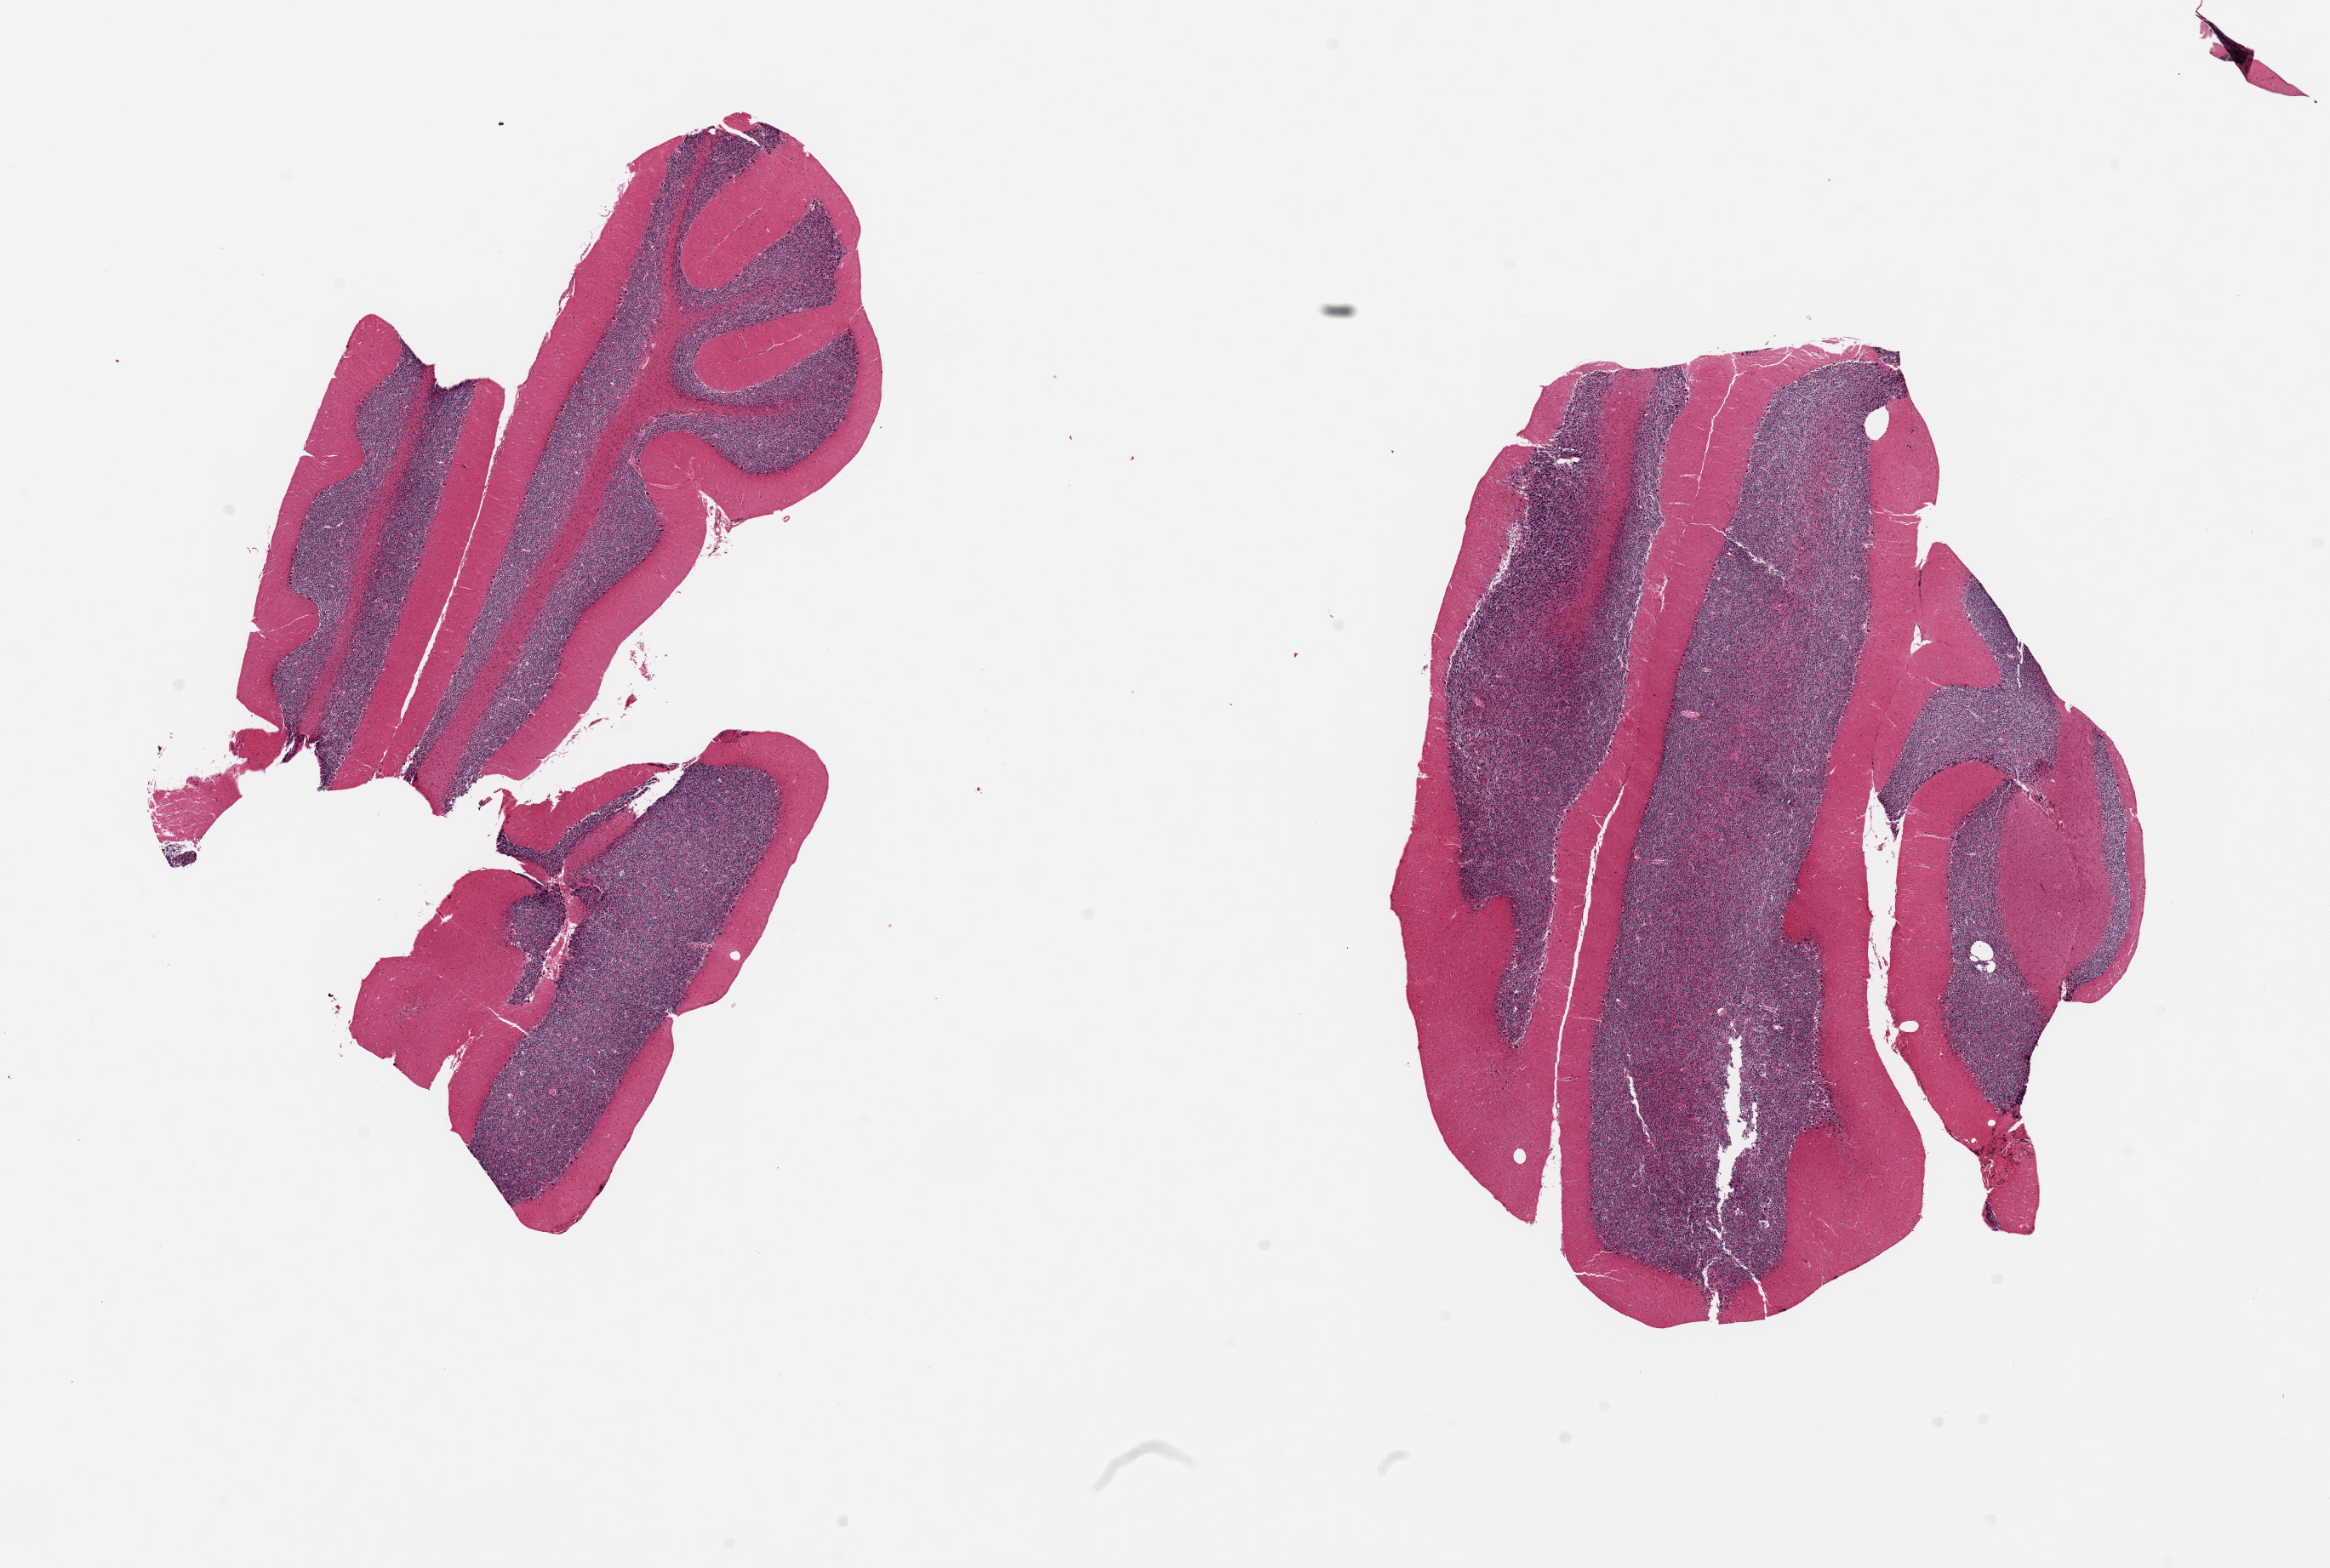
Whole-slide image, haematoxylin and eosin stain, brightfield, shown as a low-resolution overview of the whole scanned area (about 21.7 x 14.6 mm). PAXgene-fixed, paraffin-embedded tissue. Section of cerebellum (target tissue). Donor tissue sample. Donor: male.
Pathologist's review note for this sample: 3 pieces (fragmented); cerebellum, not cortex.